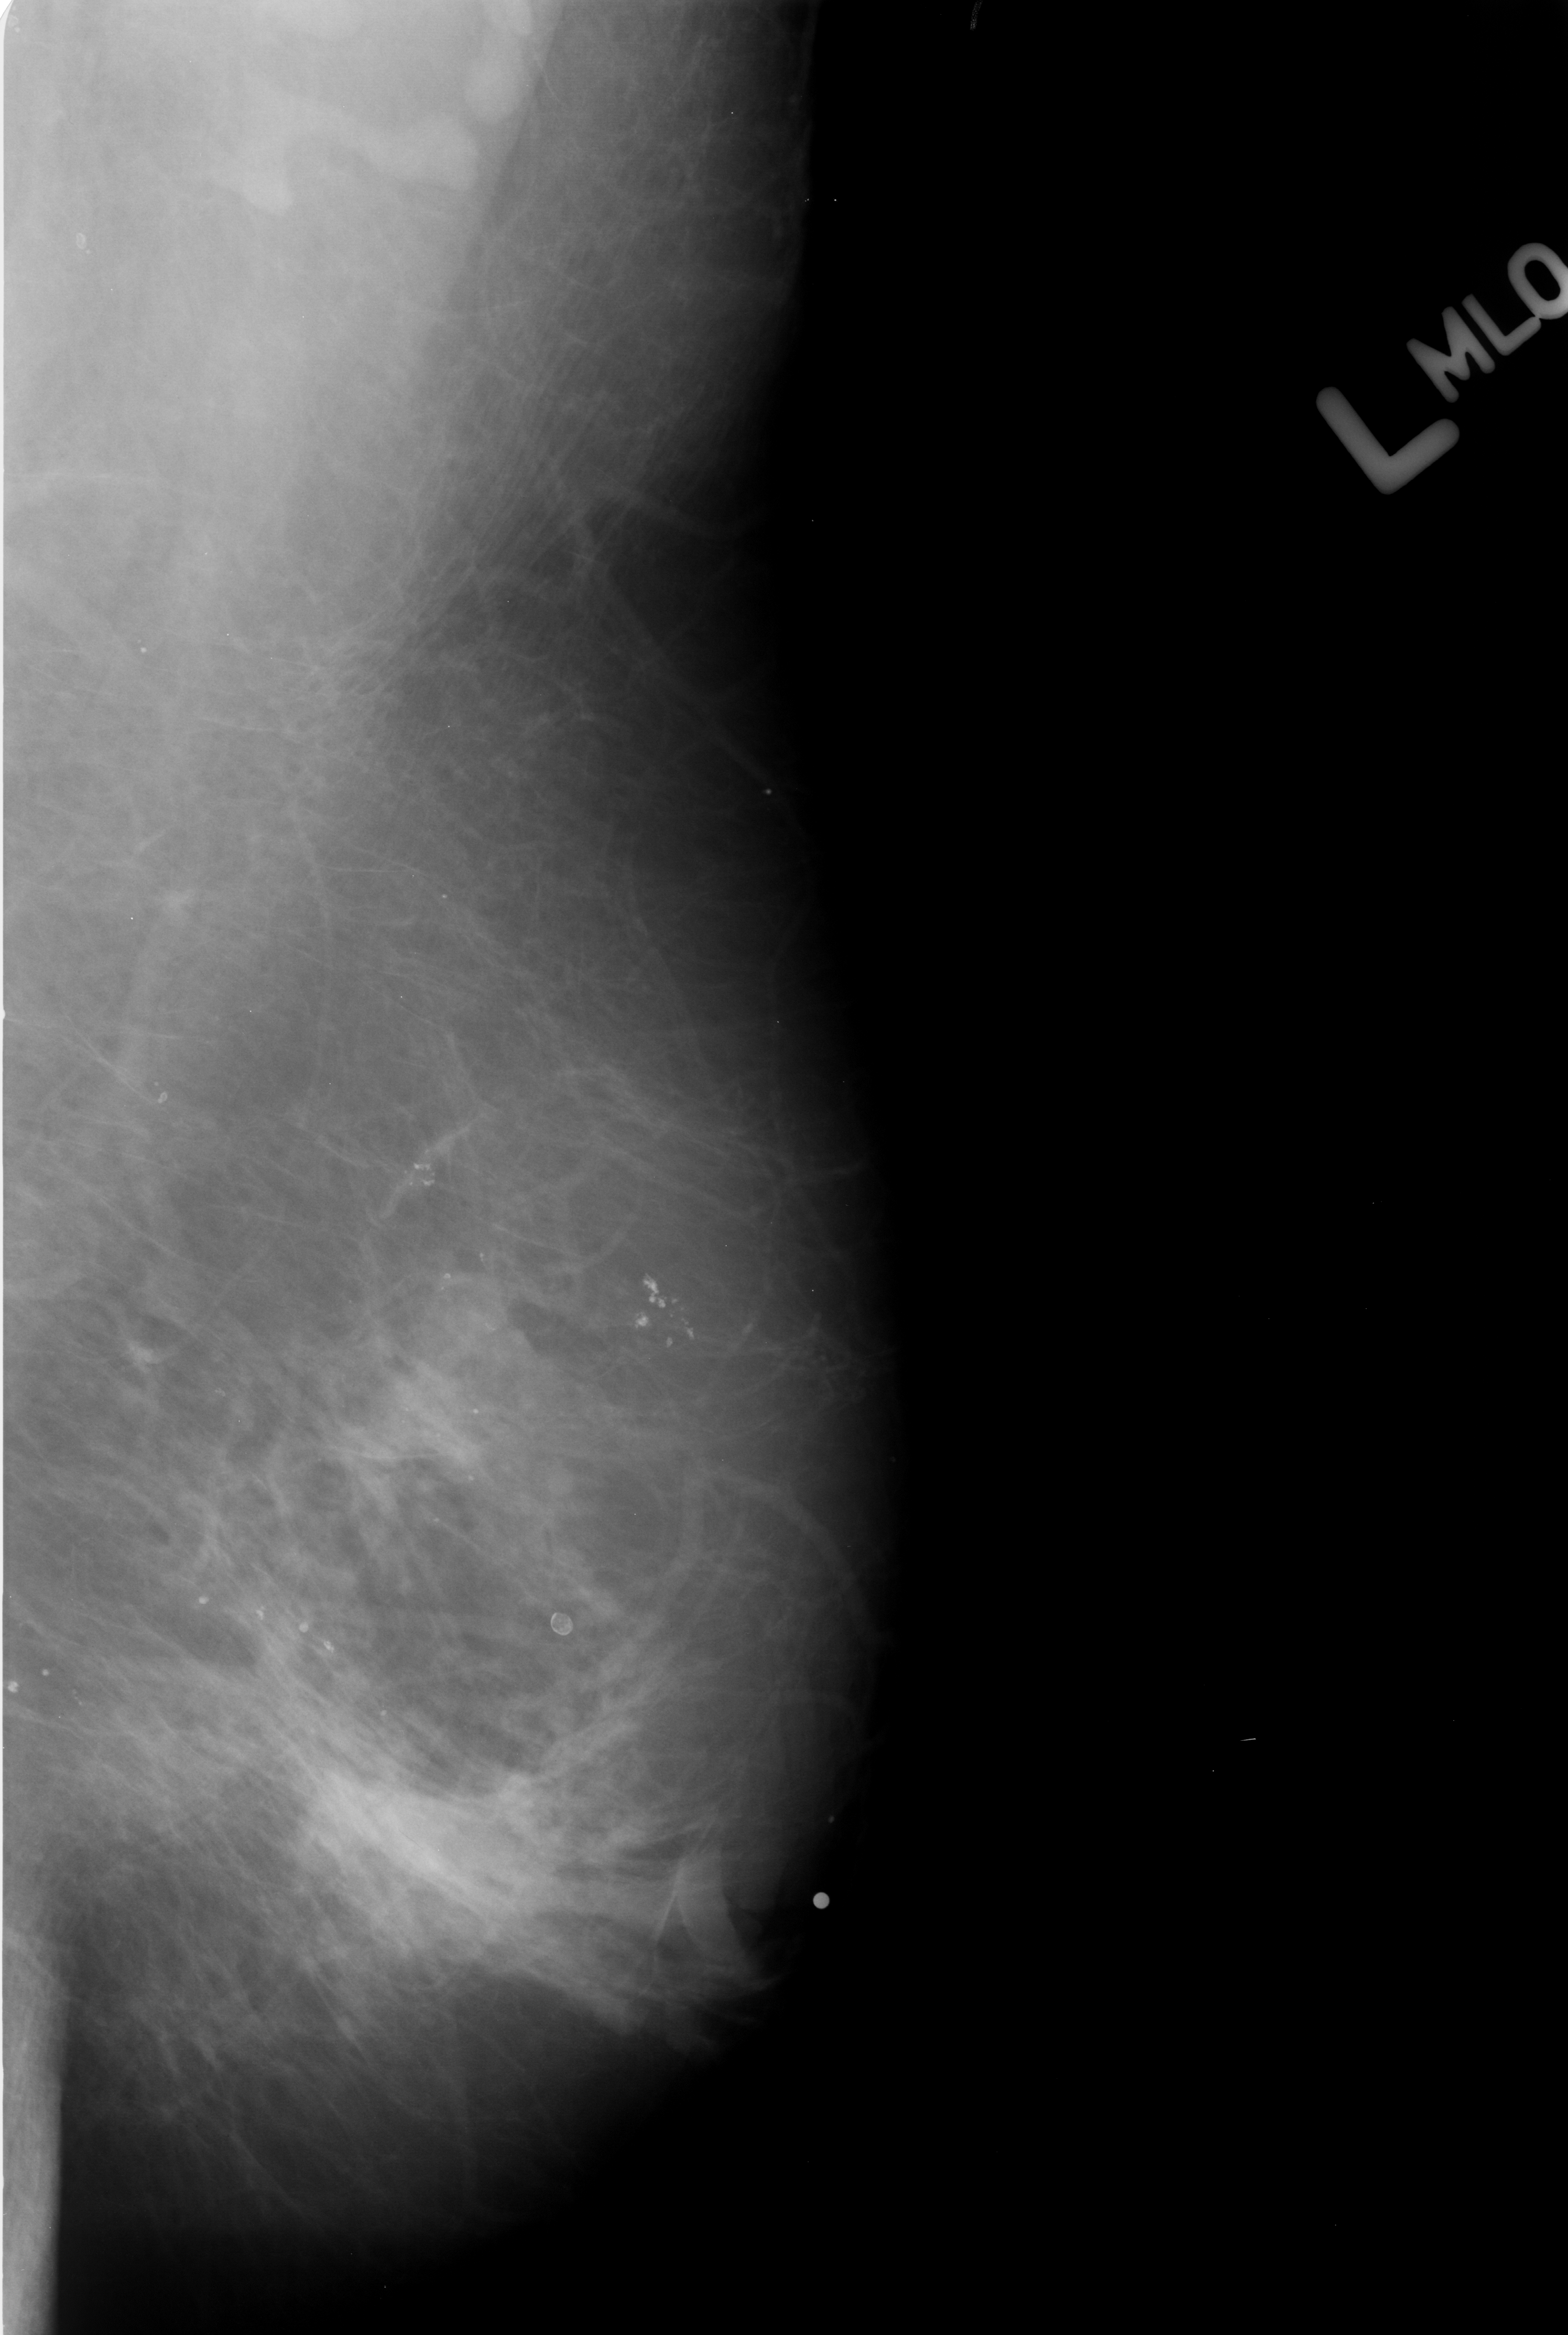
Digitized screen-film mammogram; left breast; MLO view; 1568 × 2335 image matrix.
Expert-marked regions of interest on this image (one box per marked abnormality):
- calcifications, morphology pleomorphic, distribution clustered; BI-RADS assessment category 4; subtlety rating 3 on a 1 (subtle) to 5 (obvious) scale; pathology (as recorded): benign: bounding box <385,1131,479,1225> (left, top, right, bottom; pixels)